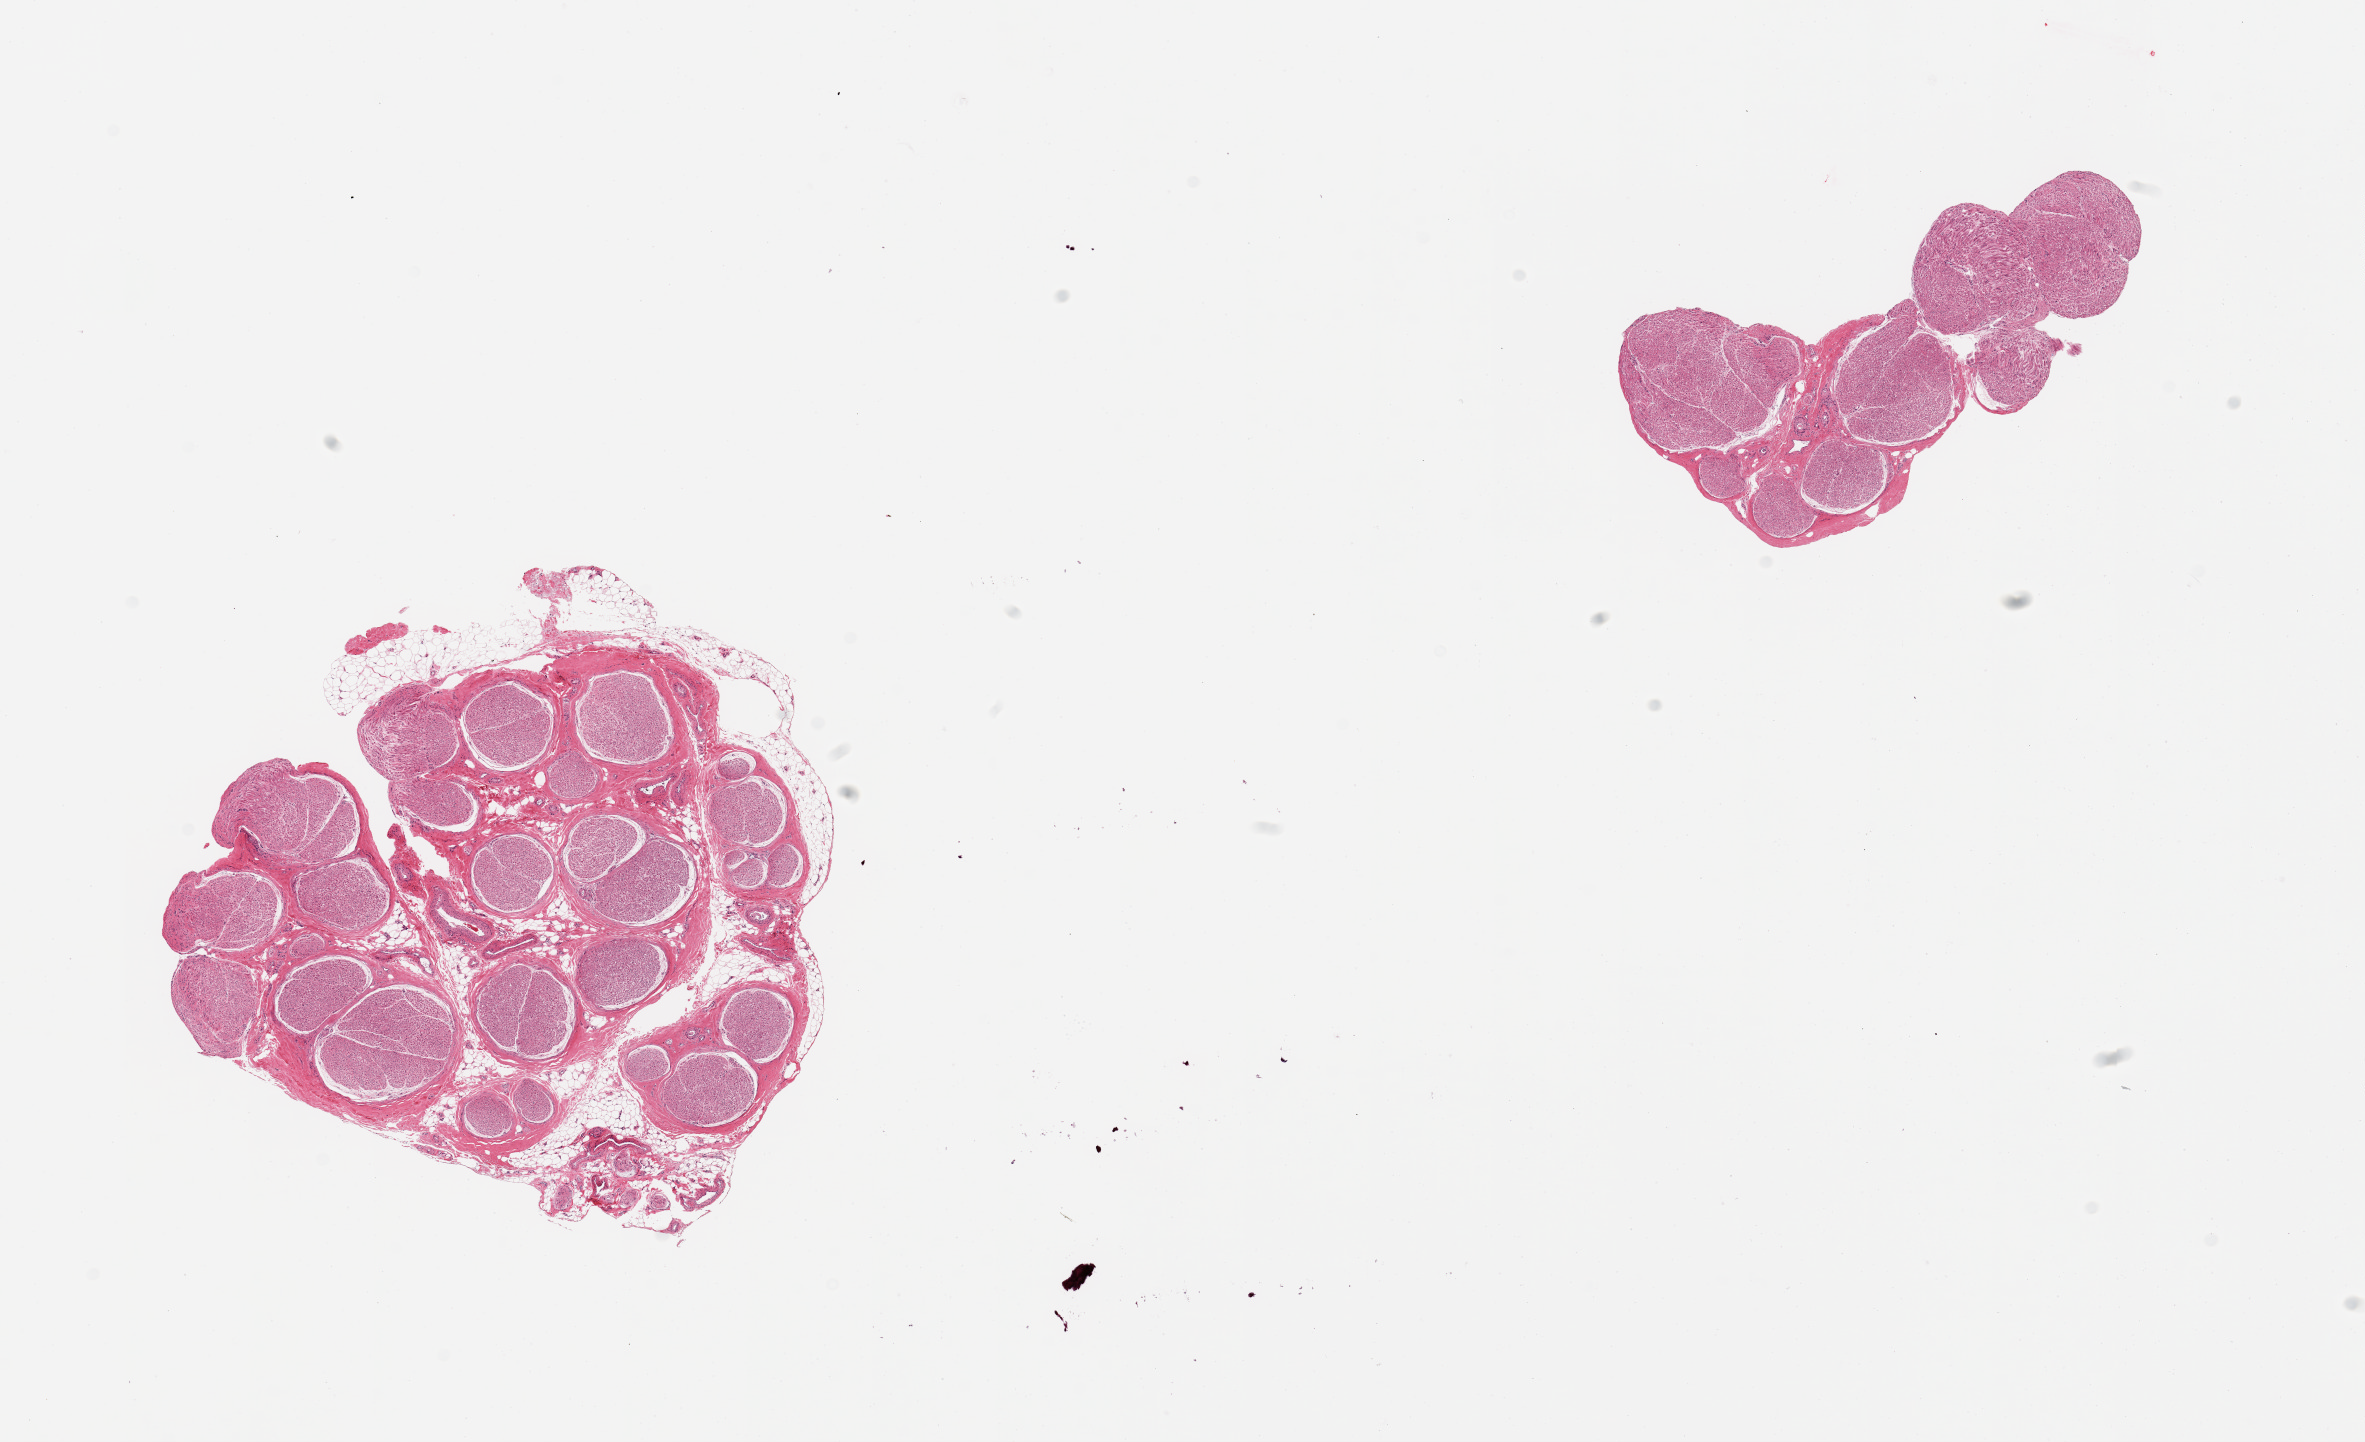
Digitized haematoxylin and eosin-stained section, brightfield — a low-resolution overview of the entire scanned area, about 18.7 x 11.4 mm (from a 20x scan). PAXgene-fixed, paraffin-embedded tissue. Section of tibial nerve (target tissue). Donor tissue sample.
* pathologist's review note for this sample: 2 pieces, partial rim of fat on one section ~0.4mm, generally clean sections